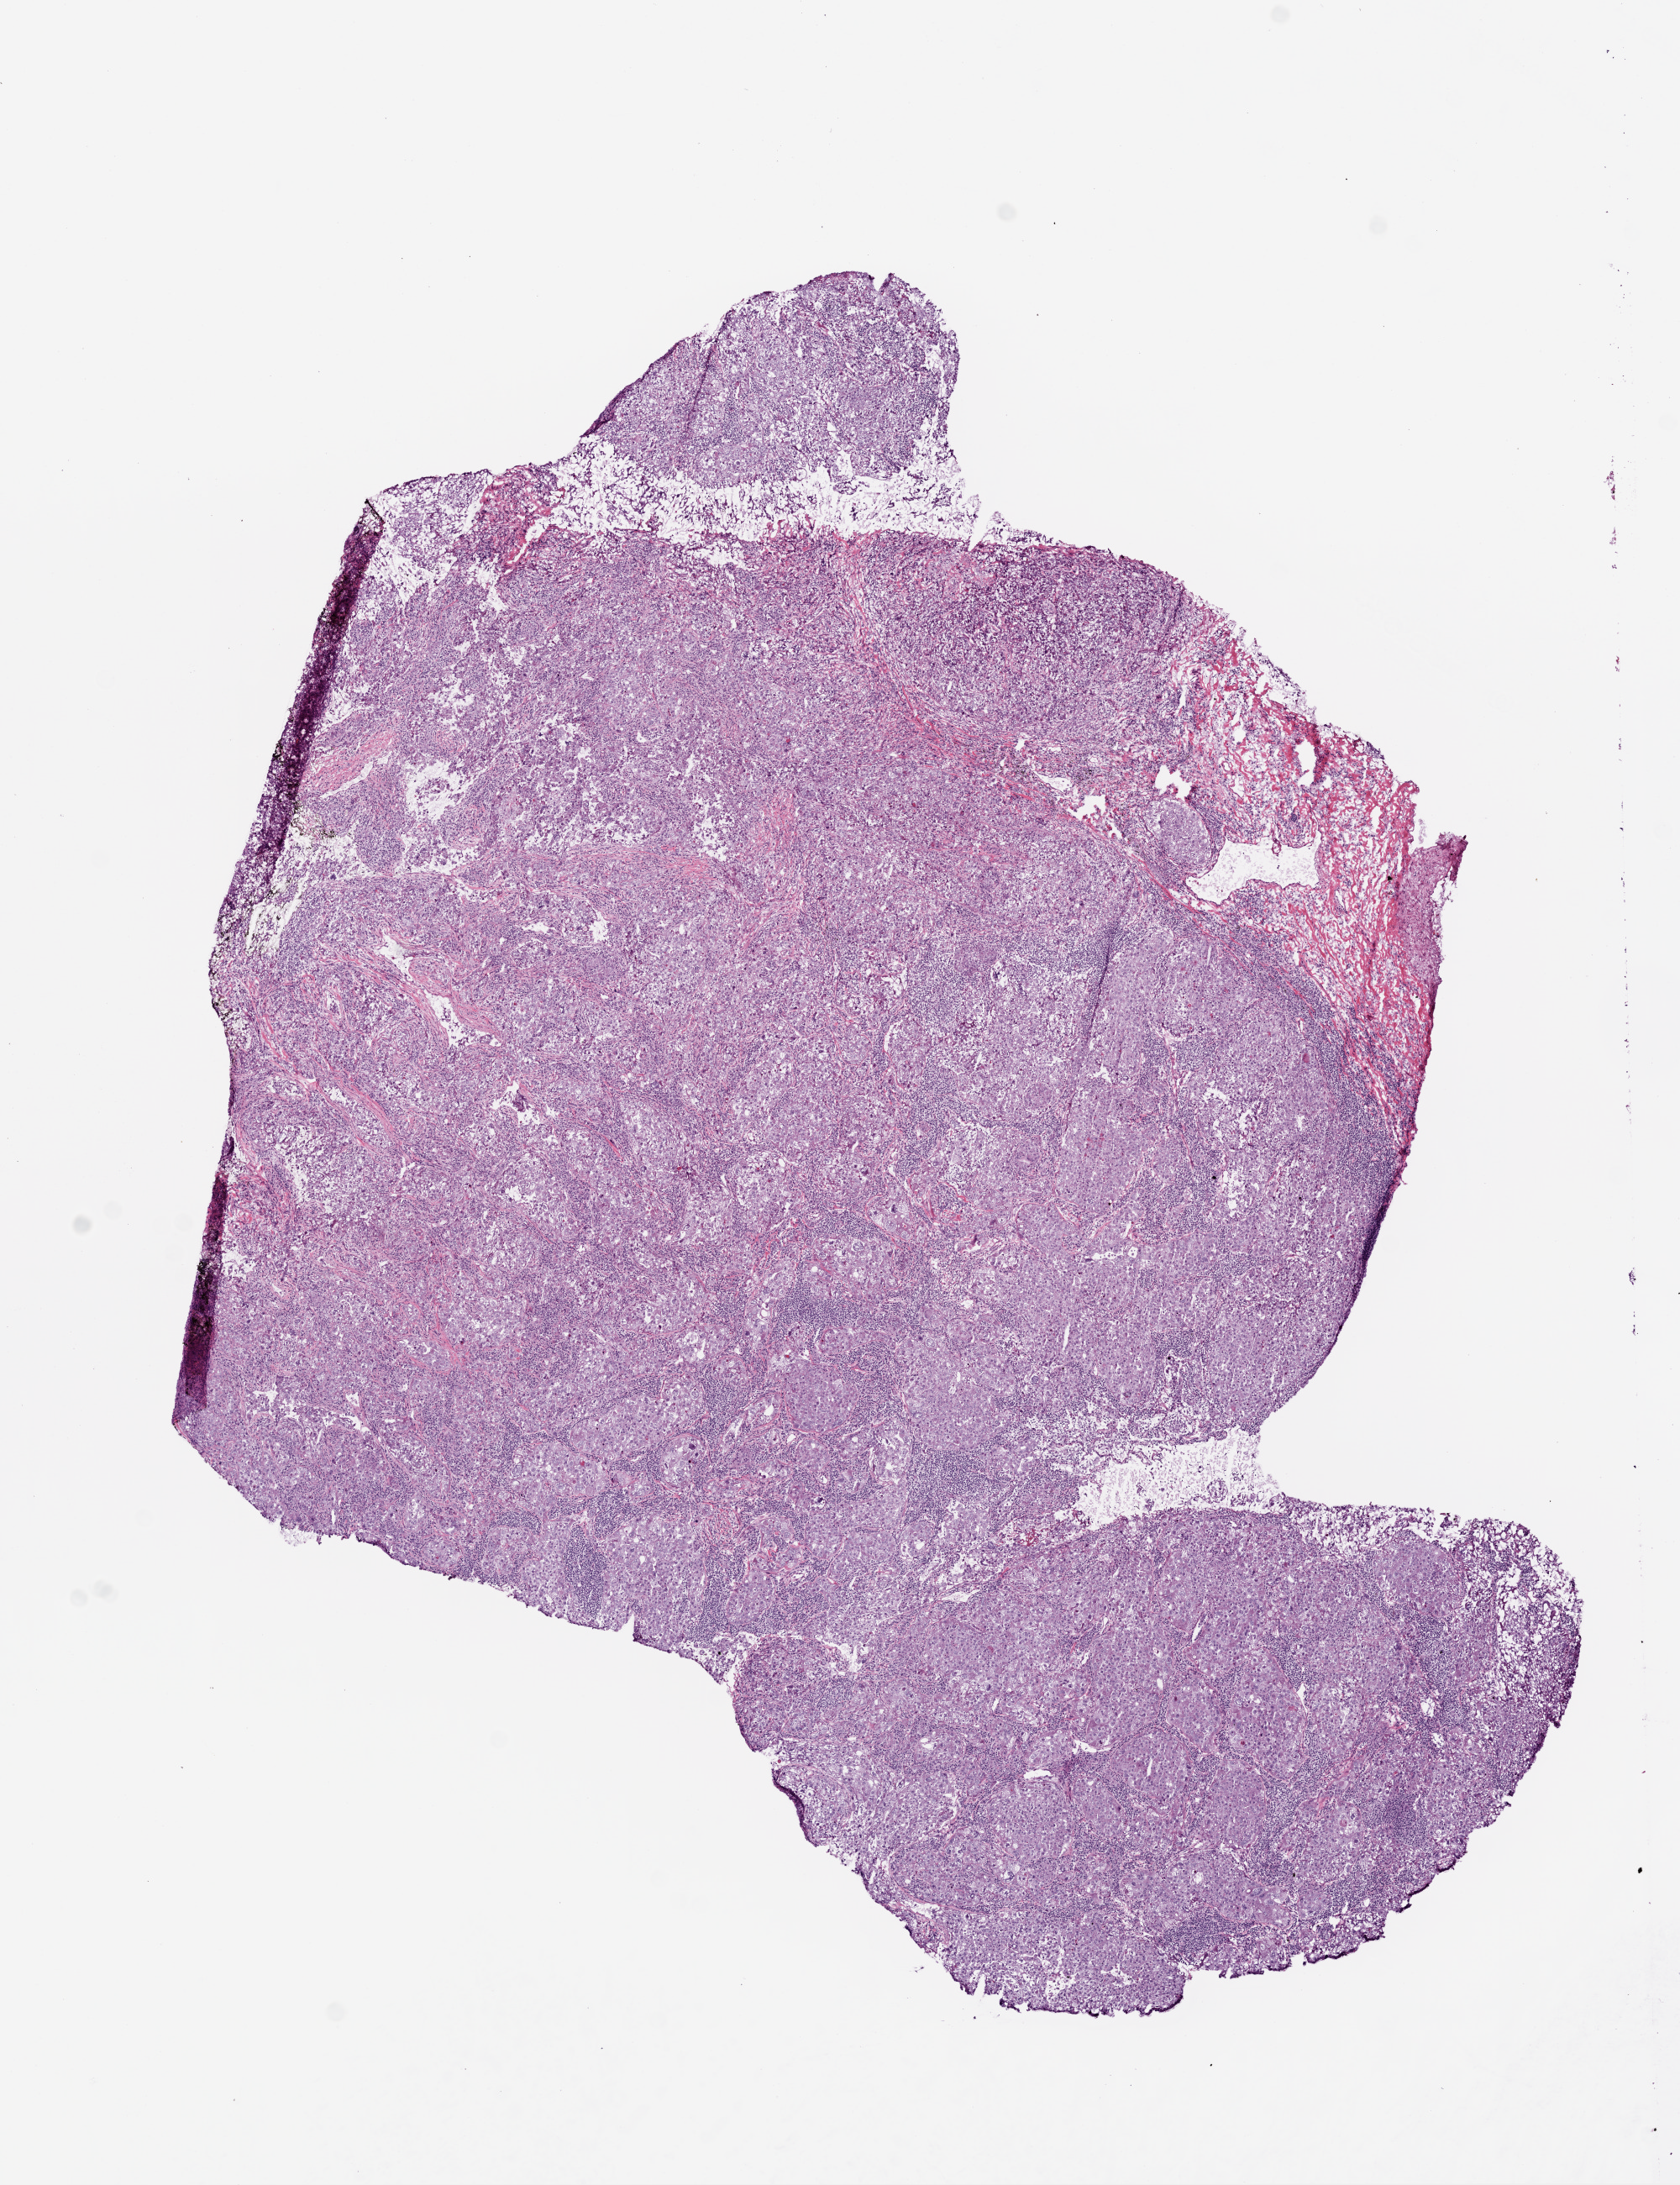
Whole-slide histology image, H&E — a low-resolution overview of the entire scanned area, about 8.0 x 10.4 mm (slide scanned at 20x); frozen section from the top of the tissue portion; primary tumour sample from the lung. Male patient; age at initial diagnosis 78 years. Composition of this section per pathologist review: tumour cells 100%, tumour nuclei 60%, normal cells 0%, stromal cells 0%, necrosis 0%. Inflammatory infiltration, as recorded: lymphocyte infiltration 30%, monocyte infiltration 1%.
Laterality: right. Diagnosis: Squamous cell carcinoma, NOS (upper lobe, lung). AJCC pathologic stage: IIA (7th edition).